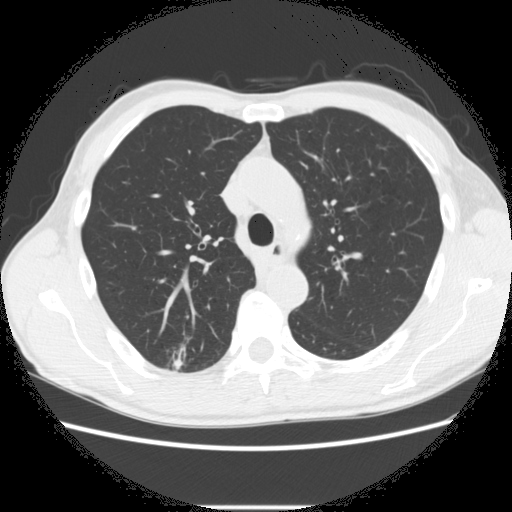
Chest CT (low-dose screening protocol), one axial image. Second screening round (one year after baseline). Lung window (W 1500 / L -600 HU). Male participant, aged 66 years at enrolment.
• Expert reader's lesion annotation, bounding box <164,341,220,381> (left, top, right, bottom; pixels).
• The screening reader recorded 5 non-calcified nodules or masses ≥4 mm on this exam (right lower lobe, right upper lobe, right upper lobe, right upper lobe, left lower lobe); which of them this box marks is not recorded.